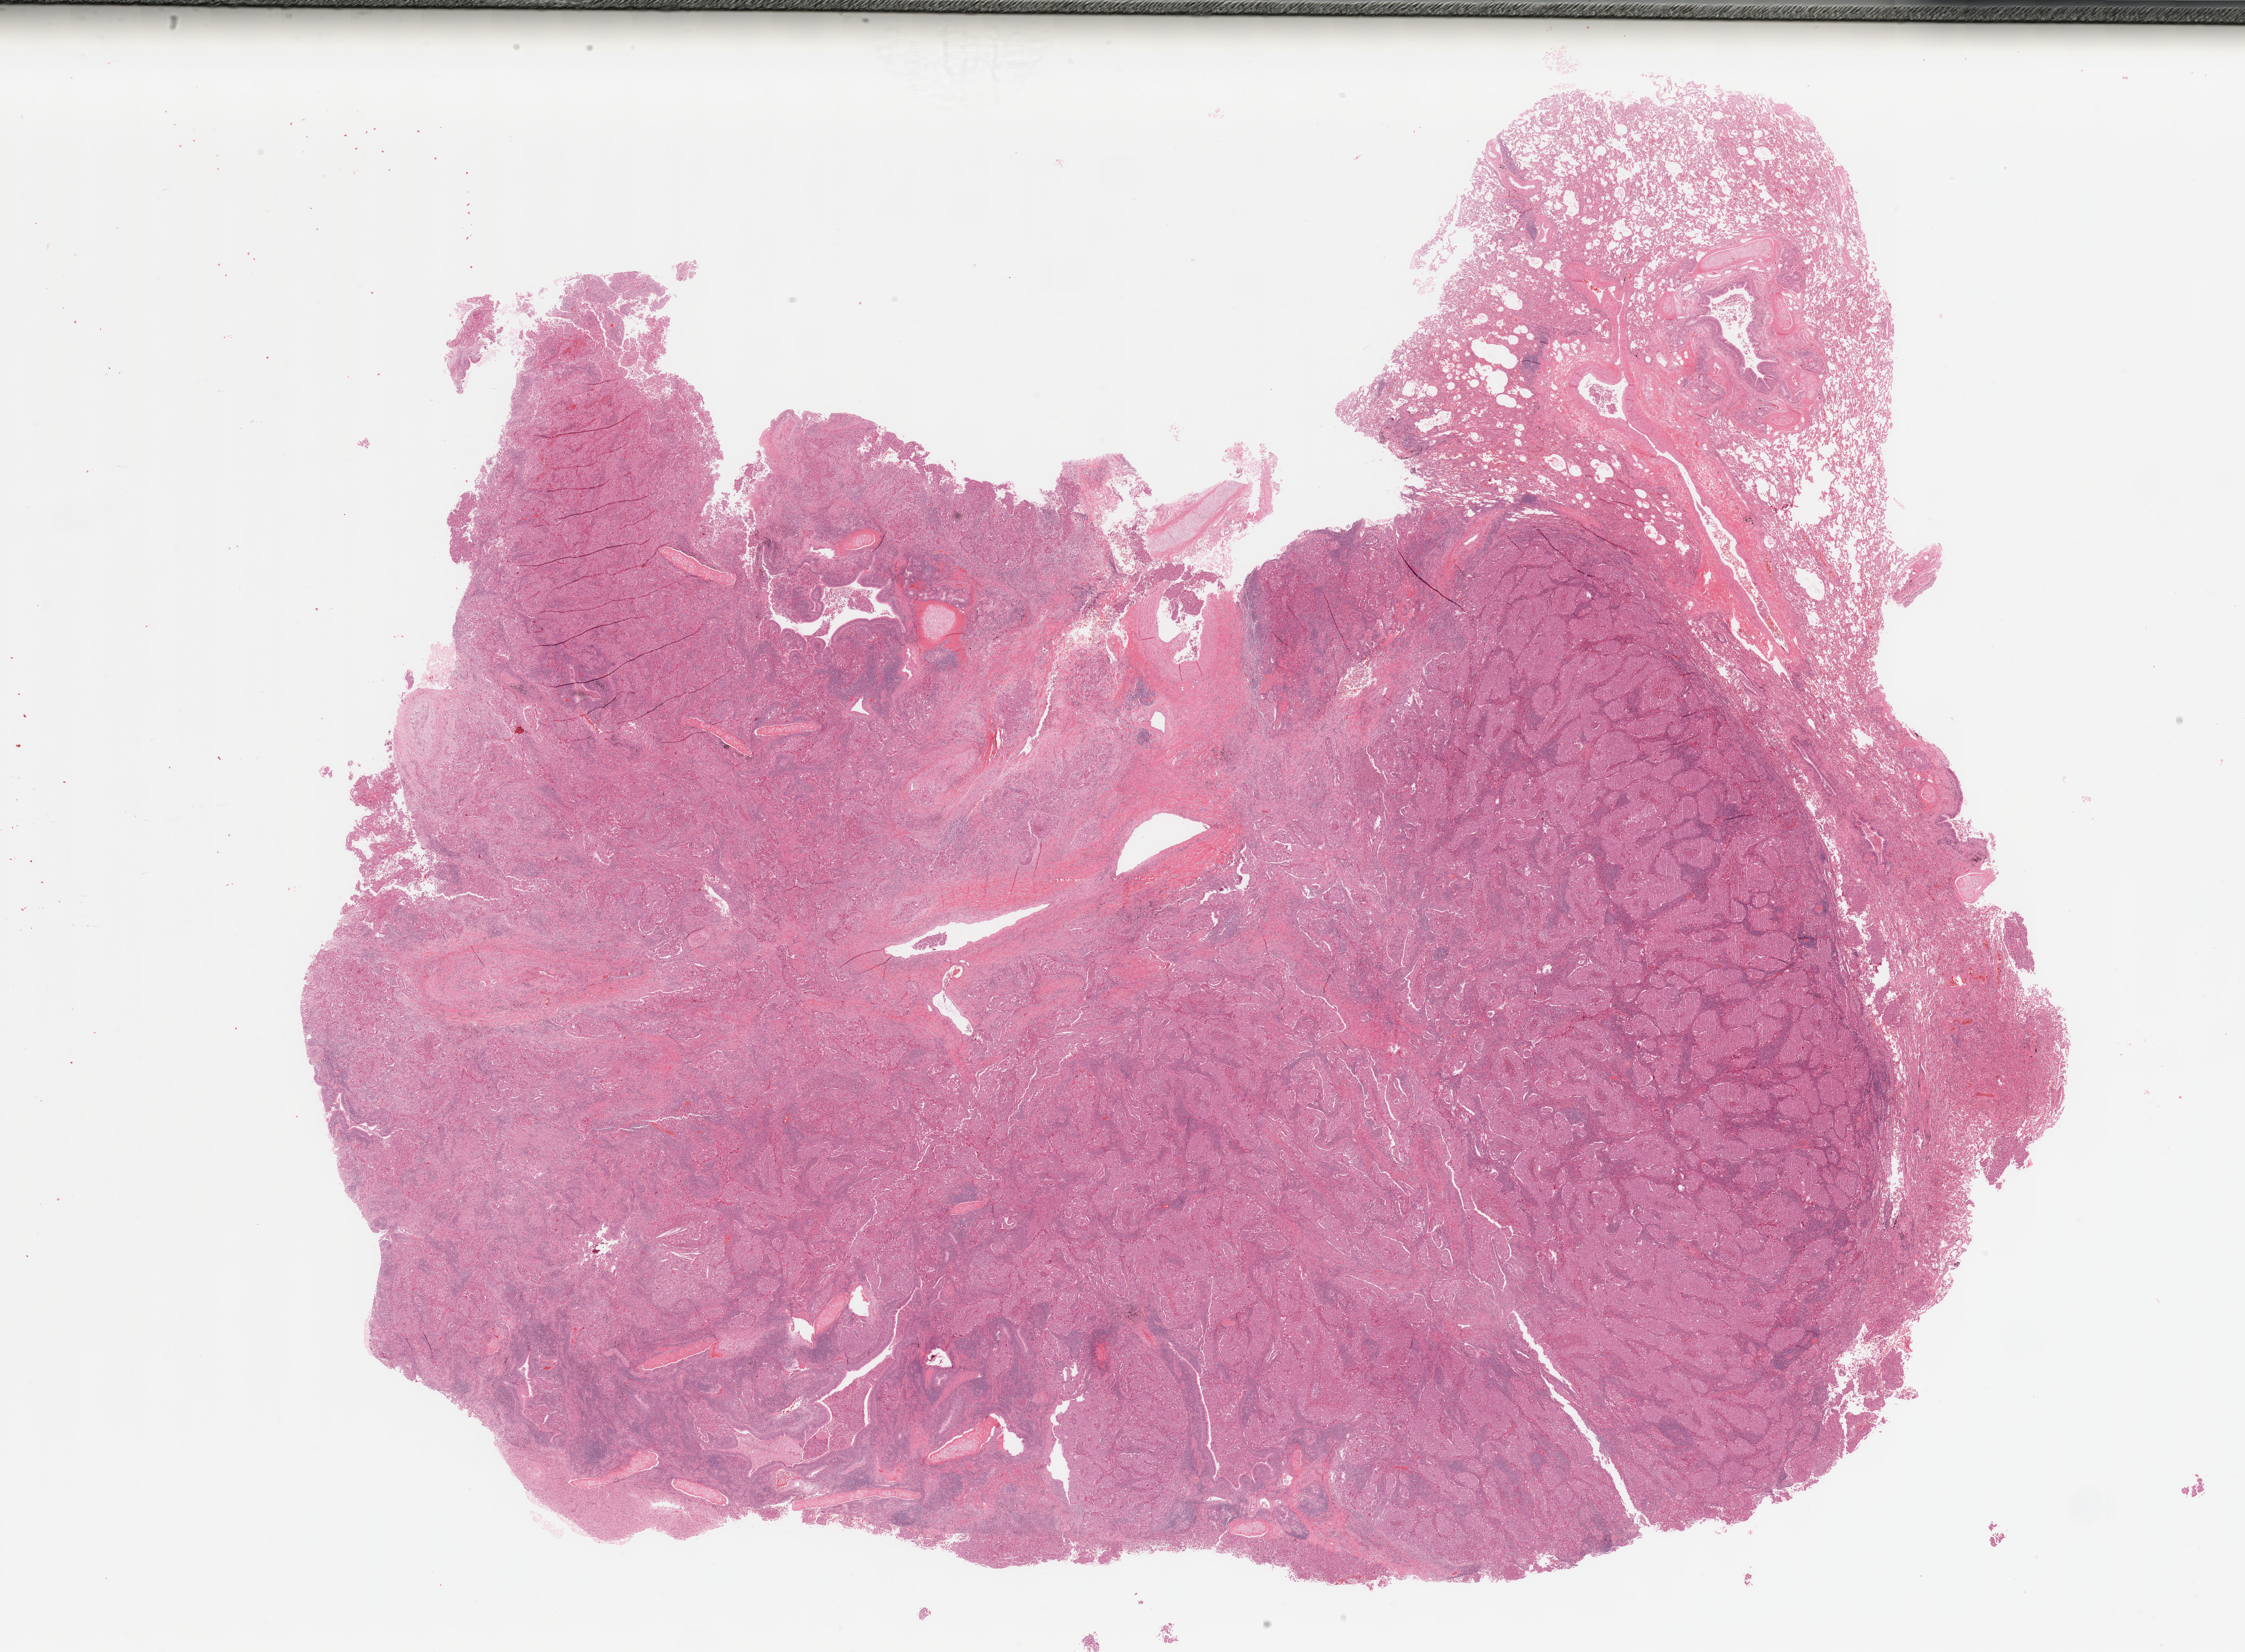
Whole-slide histology image, Hematoxylin and eosin (H&E) stained — a low-resolution overview of the entire scanned area, about 31.5 x 23.2 mm (from a 20x scan). Tumour tissue sample, lung. Female, 48 y/o. Histologic grade: G3 (poorly differentiated).
AJCC pathologic stage: IIA. Histologic diagnosis: Adenocarcinoma, NOS.